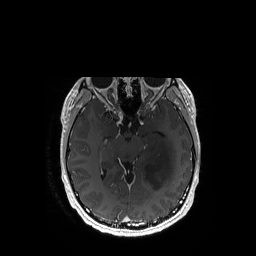
Brain MRI from a brain-tumour surgery series, one axial slice. Slice 102 of 192 in the series (ordered by position). T1-weighted post-contrast. 1 mm slice thickness. 256 × 256 image matrix. Case-level facts recorded for this patient, not image findings: histopathology: Astrocytoma; WHO grade: 3; IDH mutation: yes; tumour location: Left Temporal.
Structures marked on this image (outlined manually by an expert reader):
- tumour: bounding box <144,139,174,190> (left, top, right, bottom; pixels)